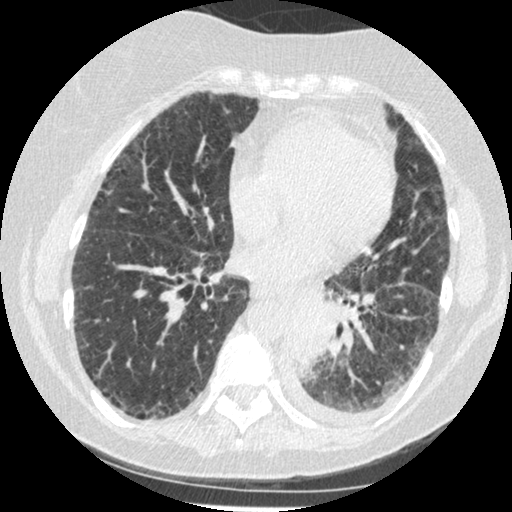
Chest CT (low-dose screening protocol), one axial image; third annual screen; lung window (W 1500 / L -600 HU); slice 251 of 341 in the series. Female participant, aged 60 years at enrolment. Former smoker at enrolment.
Expert reader's lesion annotation, bounding box <278,302,344,376> (left, top, right, bottom; pixels). The exam's reader record, not a measurement of the box and not confirmed to be the same lesion: non-calcified nodule or mass ≥4 mm, left lower lobe, 54 × 38 mm, smooth margins, soft tissue attenuation, pre-existing on the prior screen: yes; interval growth: yes. Later outcome: lung cancer diagnosed 15 days after this screen — small cell carcinoma, NOS, left lower lobe, undifferentiated (G4), stage IV (AJCC 6th edition), 69 mm at pathology.